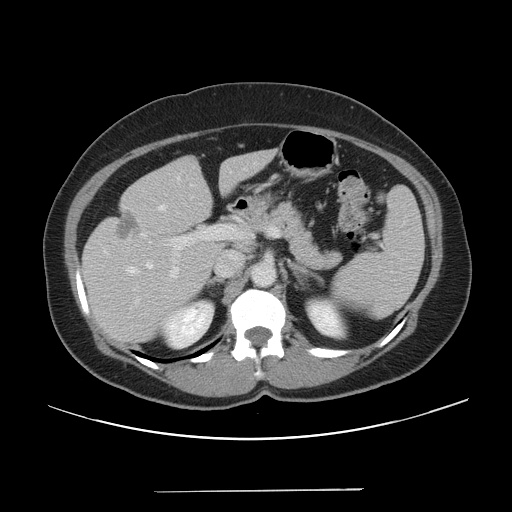
Contrast-enhanced abdominal CT, one axial slice; position 26 of 56 along the scan axis; intravenous contrast given; soft-tissue window (W 400 / L 40 HU); 512 × 512 image matrix, field of view 419 × 419 mm. Female patient, age 54 years. From the clinical record (not read from this slice): diagnosis: colorectal cancer liver metastases, imaged before liver resection; multiple liver metastases: yes; largest metastasis: 3.2 cm; disease in both lobes: yes.
Outlined on this slice (manually delineated by an expert):
- hepatic veins: box from (x=128, y=206) to (x=164, y=309) px
- liver: (x=82, y=150)–(x=276, y=346)
- planned liver remnant (the part of the liver to remain after resection): (x=170, y=150)–(x=276, y=211)
- portal vein (with intrahepatic branches): (x=170, y=226)–(x=278, y=278)
- liver metastasis: (x=116, y=209)–(x=139, y=240)